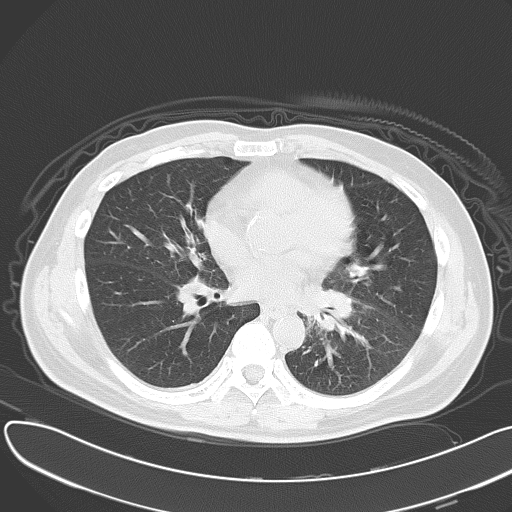
Chest CT, one axial slice. Slice 25 of 55 in the series (ordered by position). Lung window (W 1500 / L -600 HU). 512 × 512 image matrix. Patient: male, 55 years. Case-level facts recorded for this patient, not image findings: clinical TNM (as recorded): T2 N3 M0; histopathological grade: G3.
Structures marked on this image (bounding box drawn by a radiologist):
- lung tumour (recorded histology: small cell carcinoma): bounding box (x1, y1, x2, y2) in pixels: (307, 286, 360, 342)